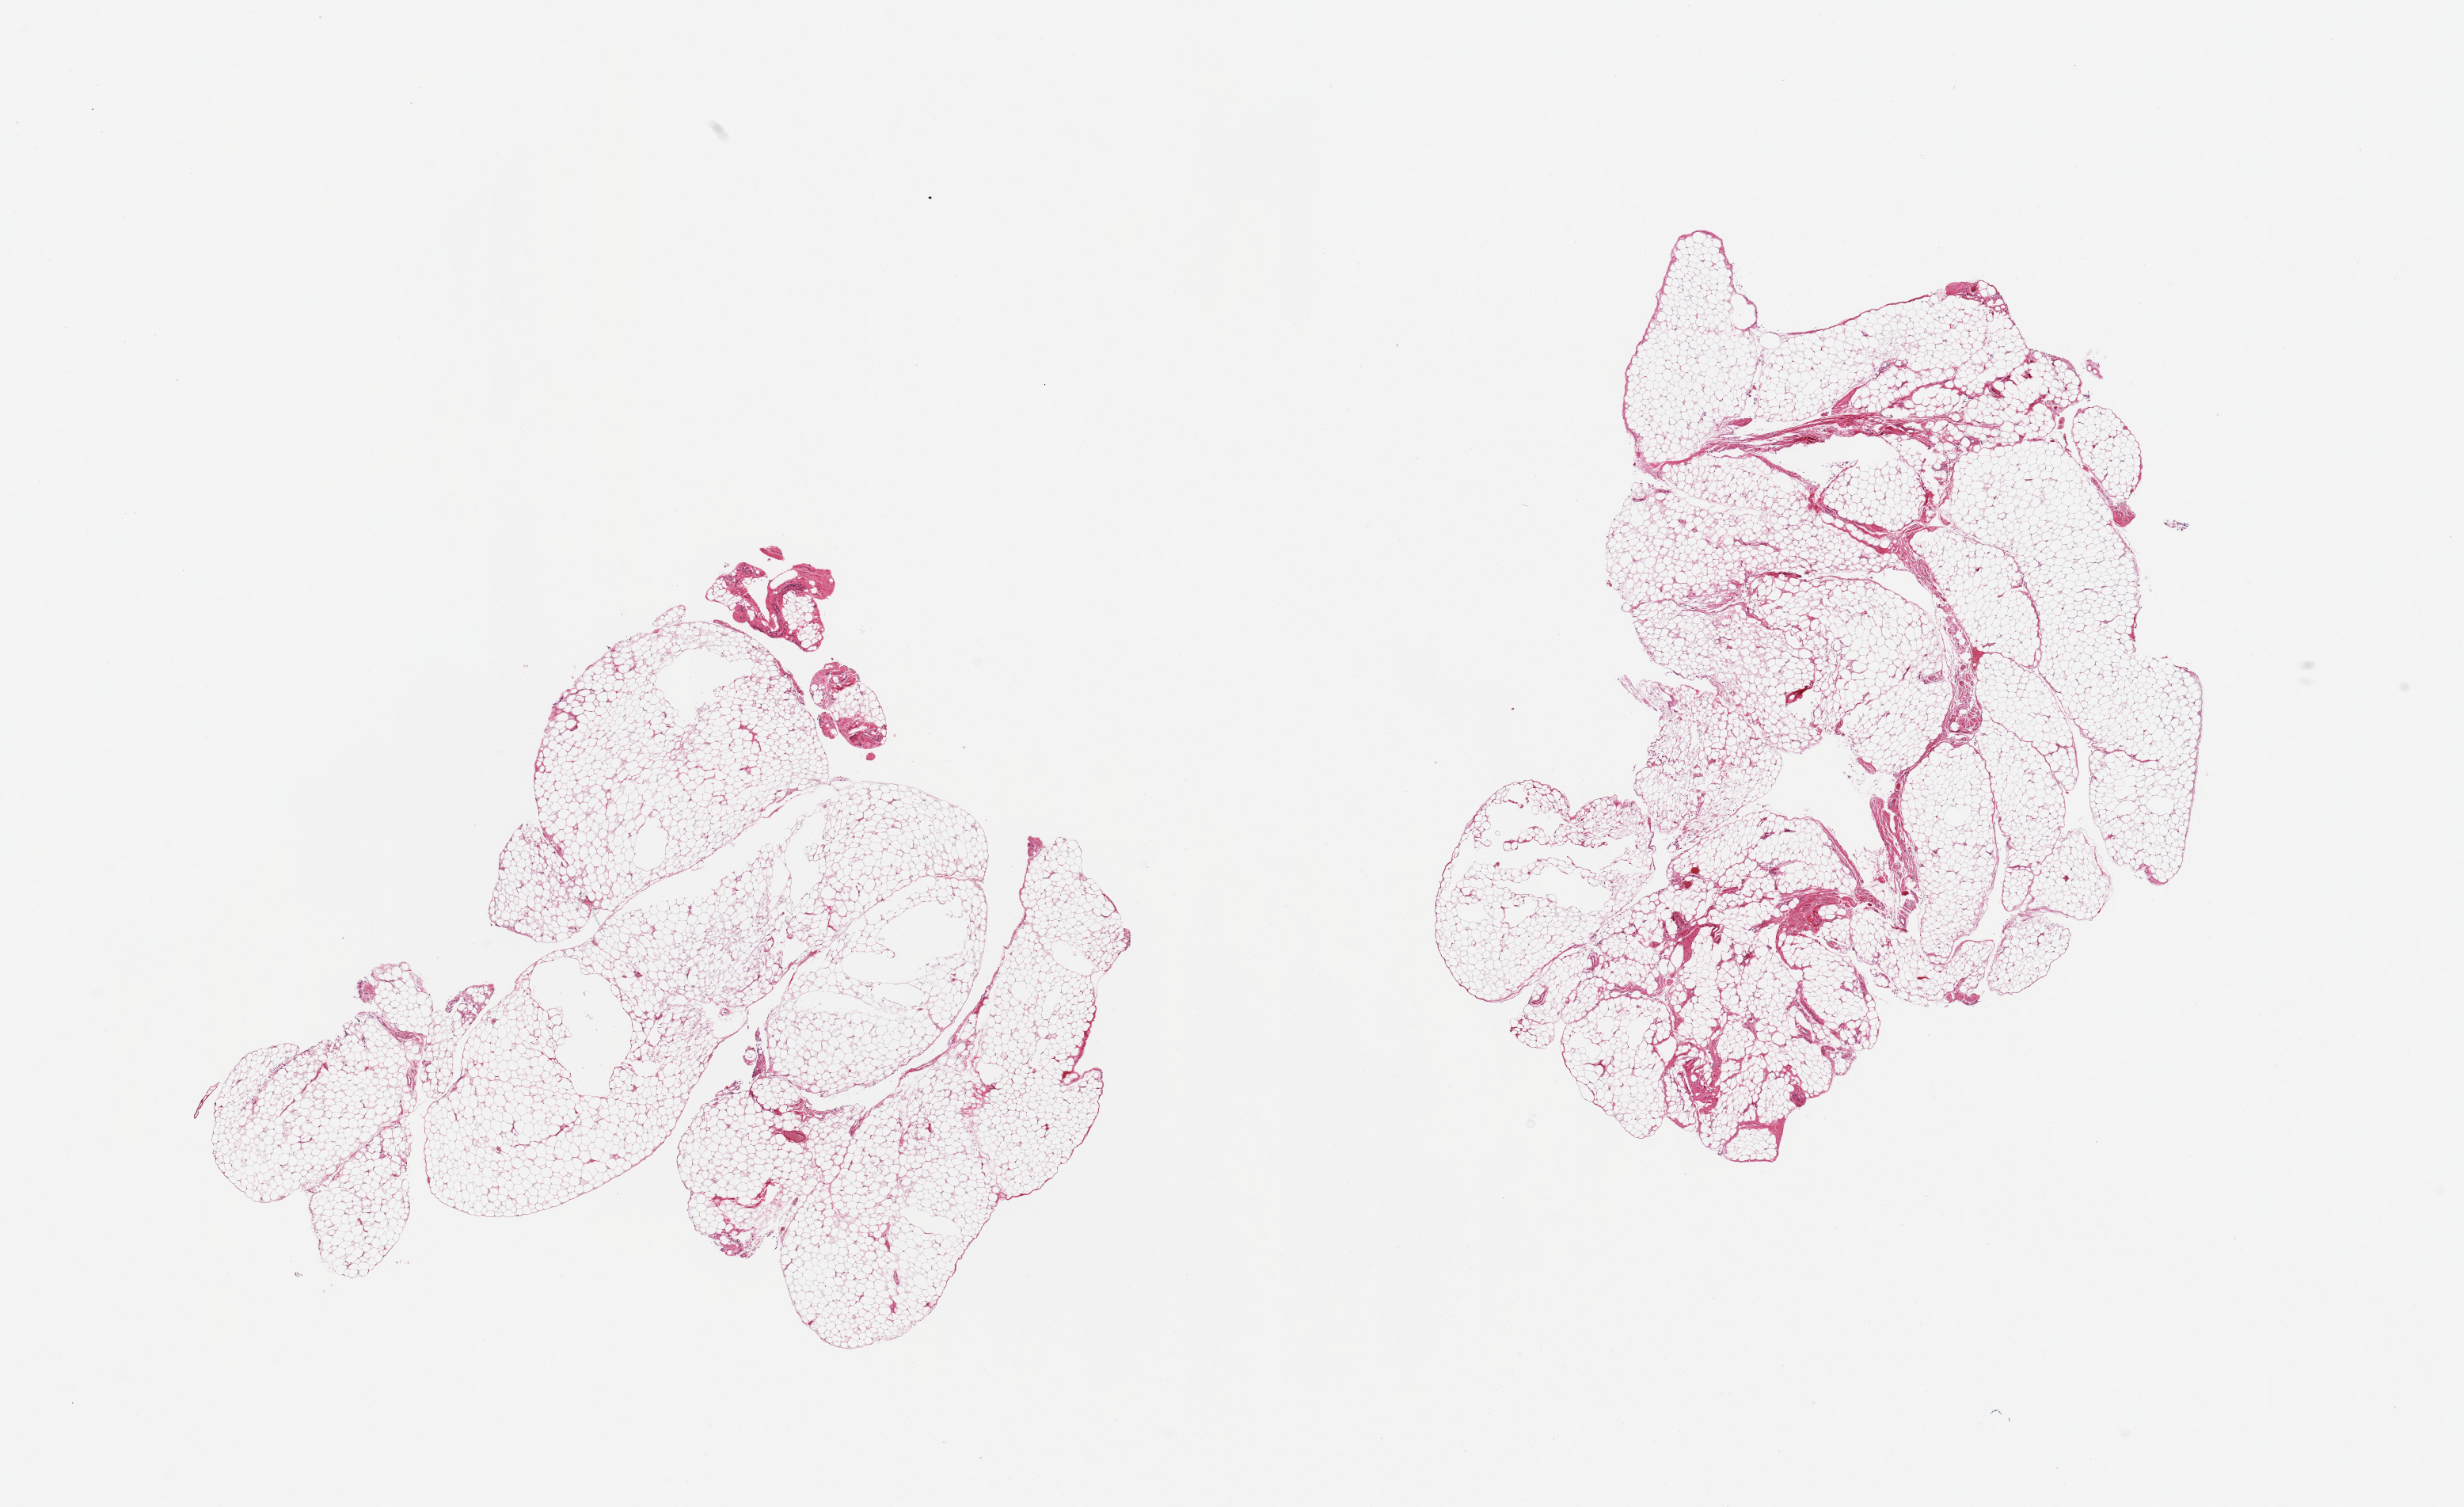
H&E whole-slide image — shown as a low-resolution overview of the whole scanned area (about 24.6 x 15.0 mm). PAXgene-fixed, paraffin-embedded tissue. Sampled site (target tissue): omentum. Tissue donor sample. Donor sex: male.
Review note (as recorded): 2 pieces, ~10% fascia/vascular elements.